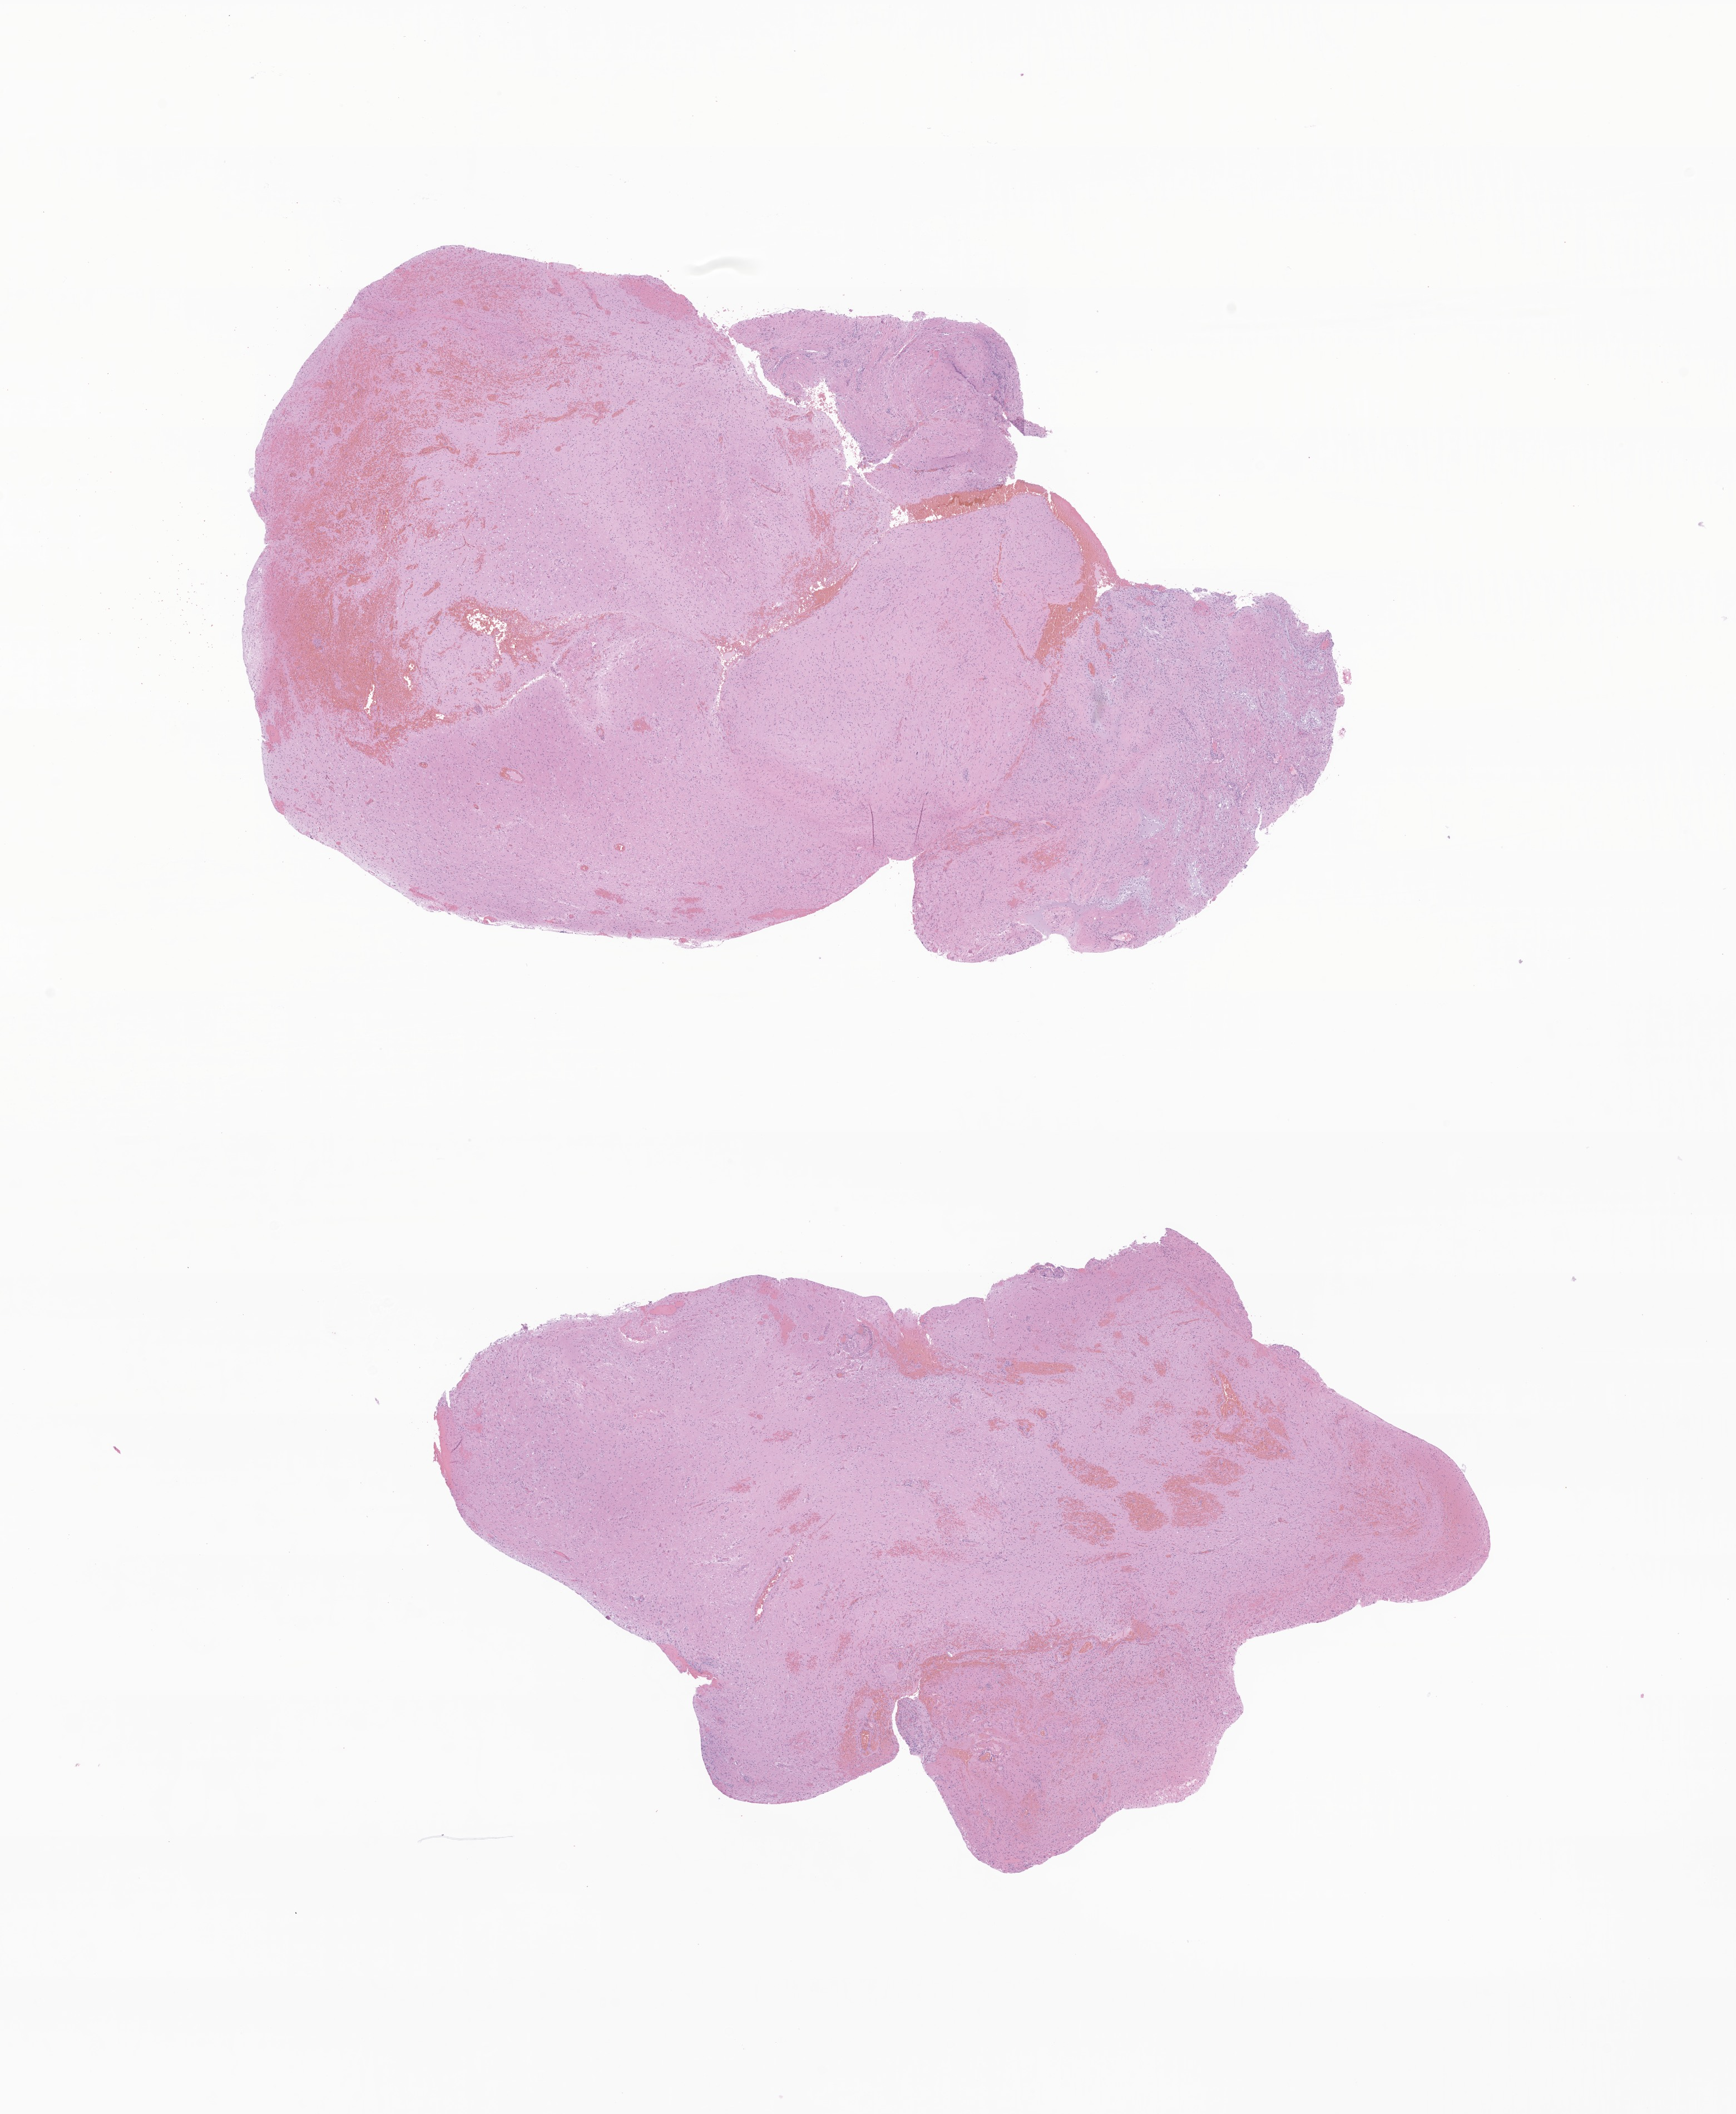
Haematoxylin and eosin whole-slide image of tumor tissue from the brain — low-resolution overview of the scanned area, about 13.2 x 16.0 mm. Formalin-fixed paraffin-embedded section. Male patient, age 192 months.
Diagnosis (ICD-O-3 morphology term): Neoplasm, uncertain whether benign or malignant.